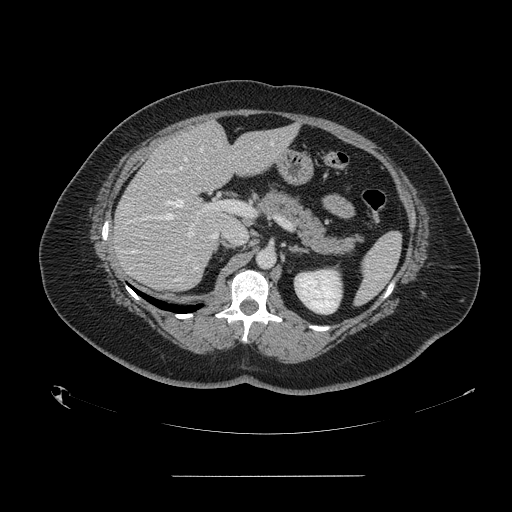
Contrast-enhanced abdominal CT, one axial slice; position 88 of 164 along the scan axis; 120 kVp; intravenous contrast given; soft-tissue window (W 400 / L 40 HU); 512 × 512 image matrix, field of view 495 × 495 mm. Female patient, age 52 years. Case-level facts recorded for this patient, not image findings: diagnosis: colorectal cancer liver metastases, imaged before liver resection; multiple liver metastases: yes; largest metastasis: 3.5 cm; disease in both lobes: no.
Outlined on this slice (expert manual segmentation):
- hepatic veins: box from (x=165, y=143) to (x=273, y=220) px
- liver: (x=114, y=123)–(x=294, y=291)
- planned liver remnant (the part of the liver to remain after resection): (x=177, y=123)–(x=295, y=224)
- portal vein (with intrahepatic branches): (x=174, y=188)–(x=244, y=236)